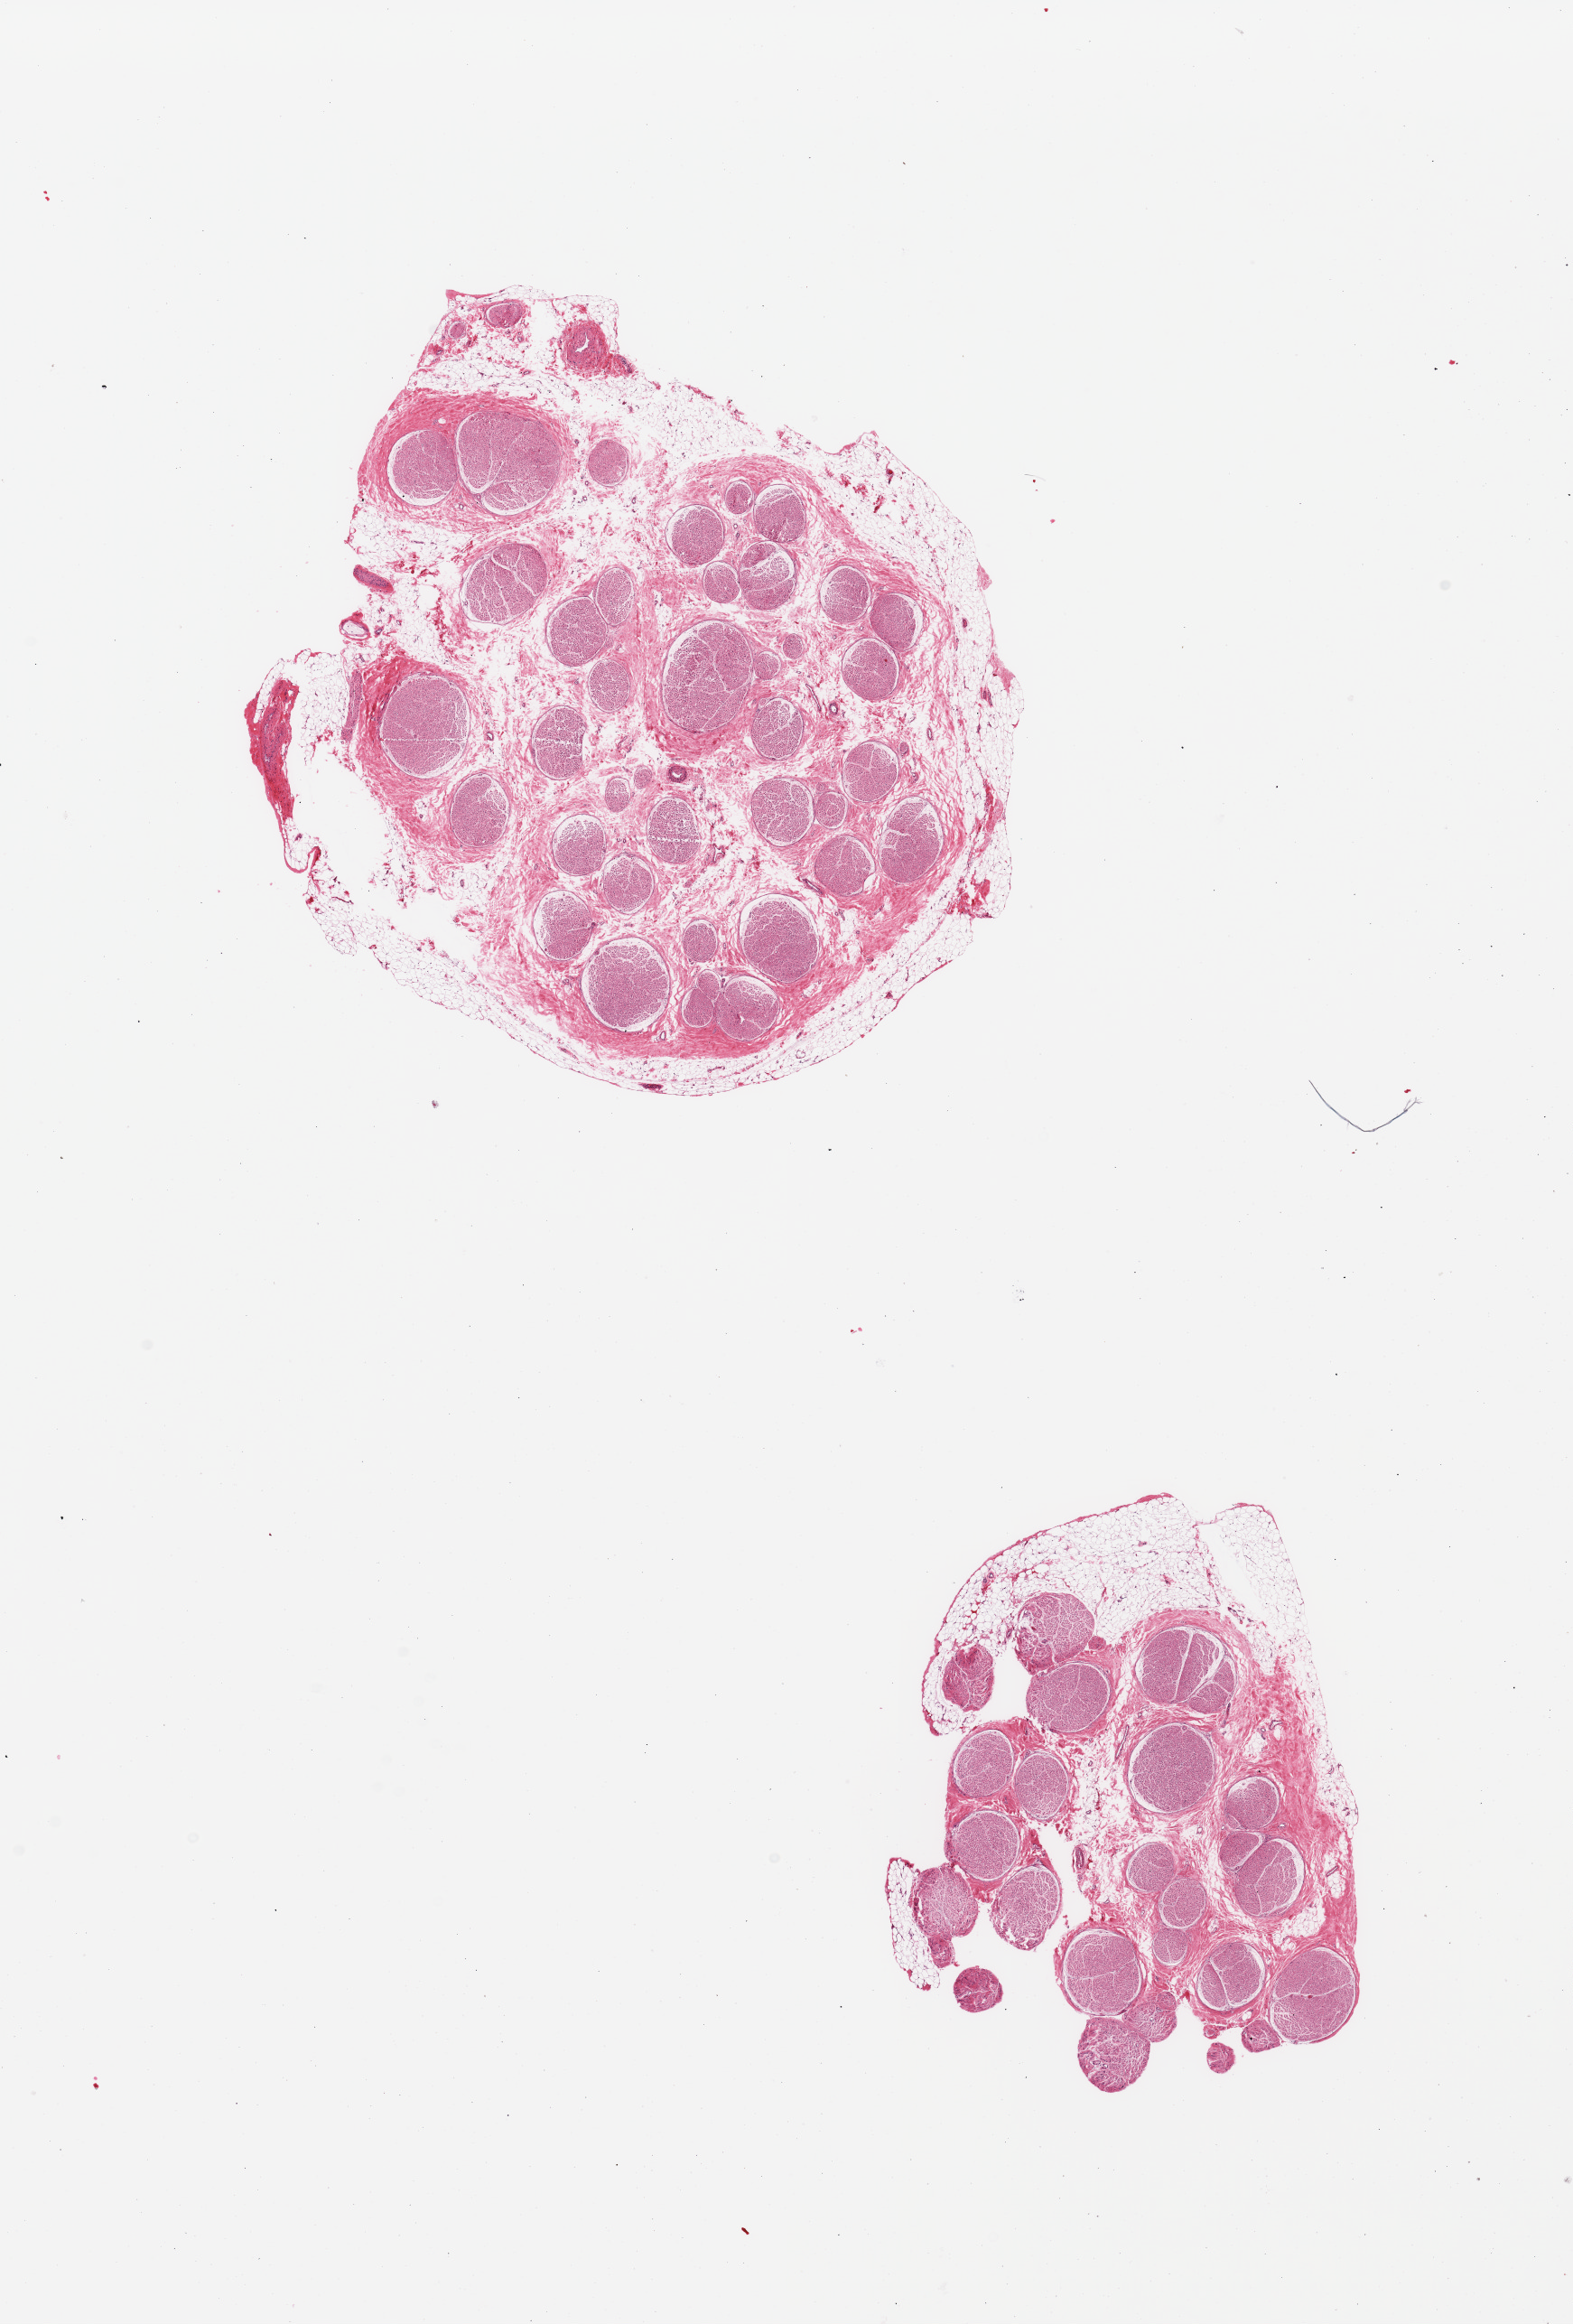
Digitized H&E-stained section — low-resolution overview of the scanned area, about 13.8 x 20.4 mm, PAXgene-fixed paraffin-embedded (PFPE) section, sampled site (target tissue): tibial nerve, tissue donor sample. Donor sex: male.
Review note (as recorded): 2 pieces; 20% internal & external fat content.